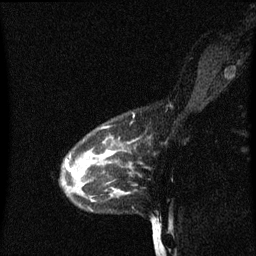
Breast MRI (dynamic contrast-enhanced), one sagittal slice; slice 47 of 60 in the series (ordered by position); dynamic contrast-enhanced series, image 2 of 3 at this slice position (ordered by acquisition); 1.5 T; TE 4.2 ms, TR 8.4 ms; 256 × 256 image matrix, field of view 200 × 200 mm. Female patient, age 38 years. Case-level facts recorded for this patient, not image findings: setting: breast cancer imaged before/during neoadjuvant chemotherapy; receptor status: HR-positive, HER2-negative.
Annotated regions visible in this slice (semi-automatic segmentation, software-assisted and operator-edited):
- analysis volume of interest (the breast-tissue region the enhancement analysis was run in; not a lesion): bounding box (x1, y1, x2, y2) in pixels: (62, 136, 133, 203)
- tumour enhancement mask (voxels above the 70 % enhancement threshold inside the analysis volume of interest): (68, 168, 71, 171)